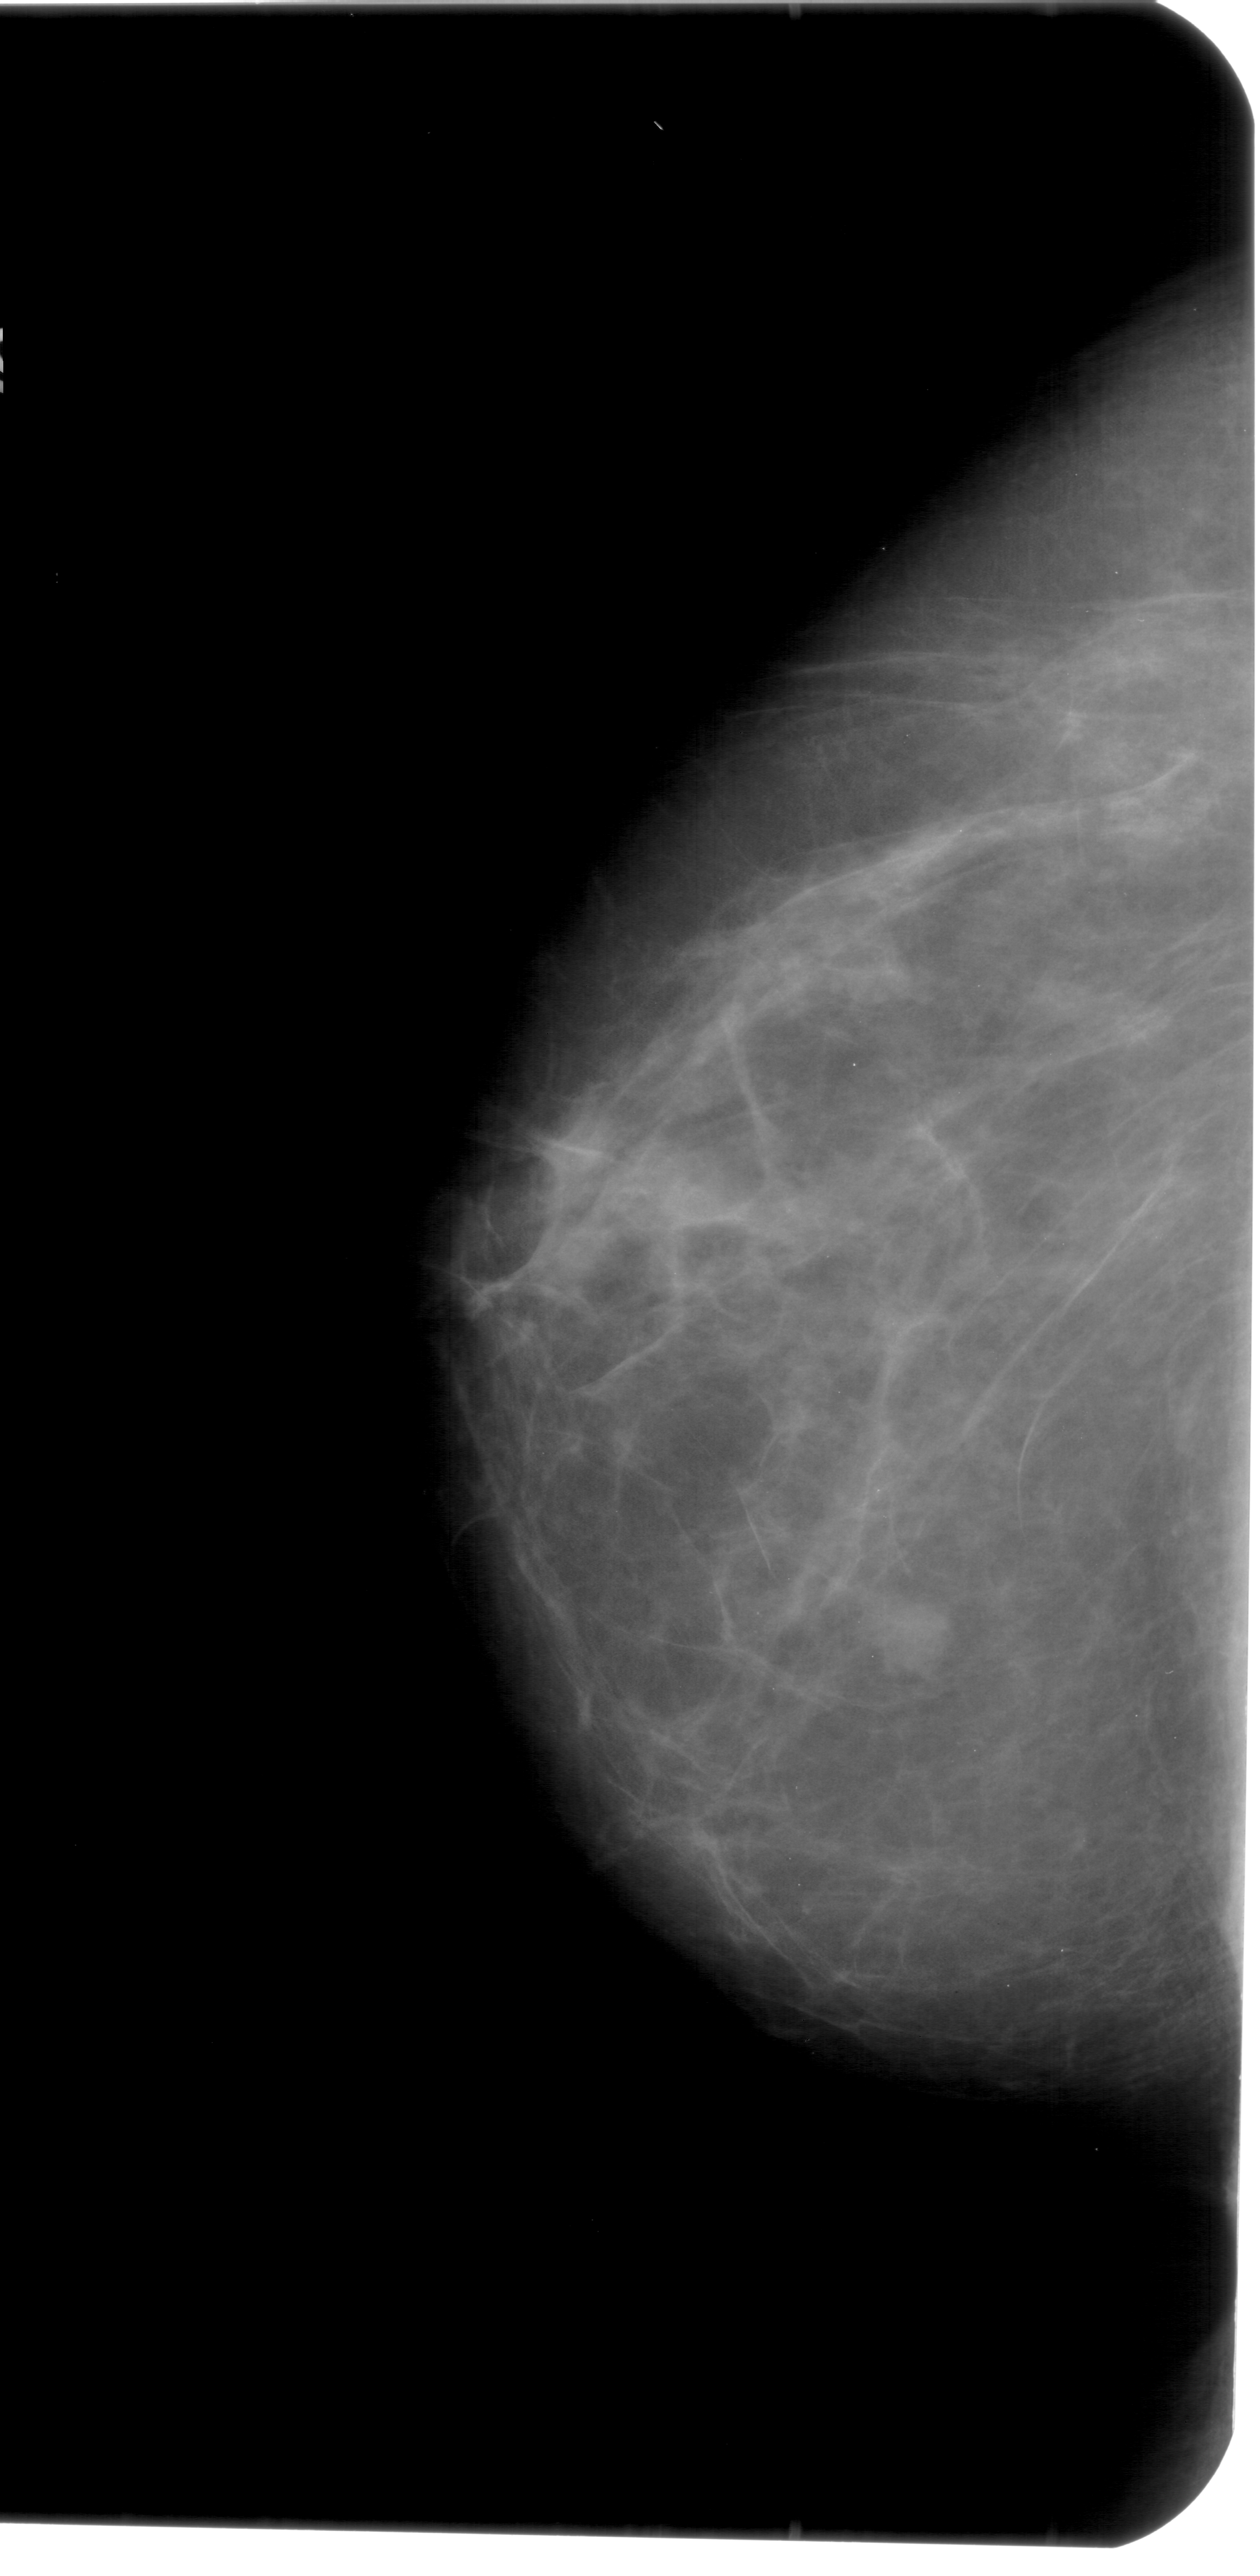
Scanned film-screen mammogram; left breast; CC view; 1260 × 2576 image matrix.
Marked abnormalities (boxes around the expert regions of interest):
- mass, shape irregular, margins ill defined; BI-RADS assessment category 4; subtlety rating 3 on a 1 (subtle) to 5 (obvious) scale; pathology result (as recorded, not read from the image): benign: bounding box (x1, y1, x2, y2) in pixels: (855, 1589, 956, 1675)